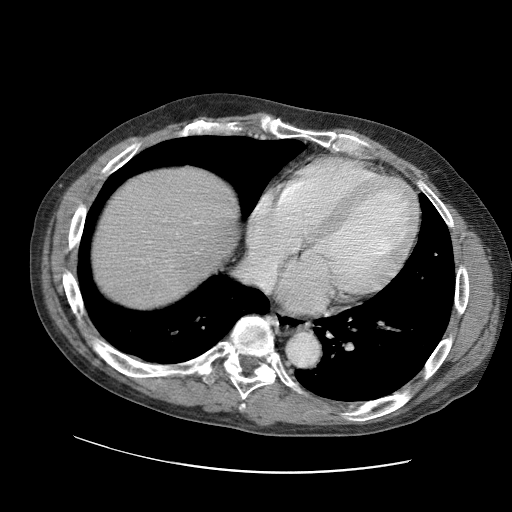
Contrast-enhanced abdominal CT (liver protocol), one axial slice; reconstruction kernel STANDARD; soft-tissue window (W 400 / L 40 HU); 2.5 mm slice thickness; 512 × 512 image matrix, field of view 400 × 400 mm. From the clinical record (not read from this slice): diagnosis: hepatocellular carcinoma (patient treated with transarterial chemoembolisation; whether this scan precedes or follows treatment is not stated here); TNM stage (as recorded): Stage-IIIC; Child-Pugh class: B; tumour differentiation: well differentiated; tumour nodularity: uninodular.
Outlined on this slice (semi-automatically segmented with operator editing):
- liver parenchyma outside the tumour (the mass and vessels are separate outlines, so this box may not span the whole liver): bounding box (x1, y1, x2, y2) in pixels: (90, 164, 238, 310)
- liver vessels: (141, 214, 201, 264)